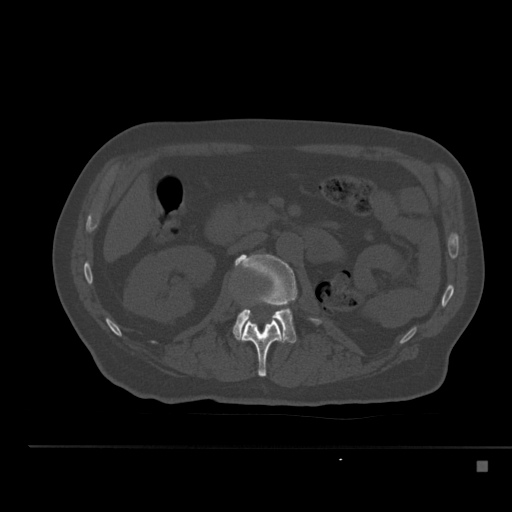
CT including the spine, one axial slice. Slice 197 of 517 in the series (ordered by position). 120 kVp. Bone window (W 1800 / L 400 HU). 512 × 512 image matrix, field of view 408 × 408 mm. Patient: male, 70 years. Case-level facts recorded for this patient, not image findings: primary cancer: renal.
Outlined on this slice (semi-automatically segmented with operator editing):
- L1 vertebra: bounding box <239,318,286,377> (left, top, right, bottom; pixels)
- L2 vertebra: <233,254,320,343>